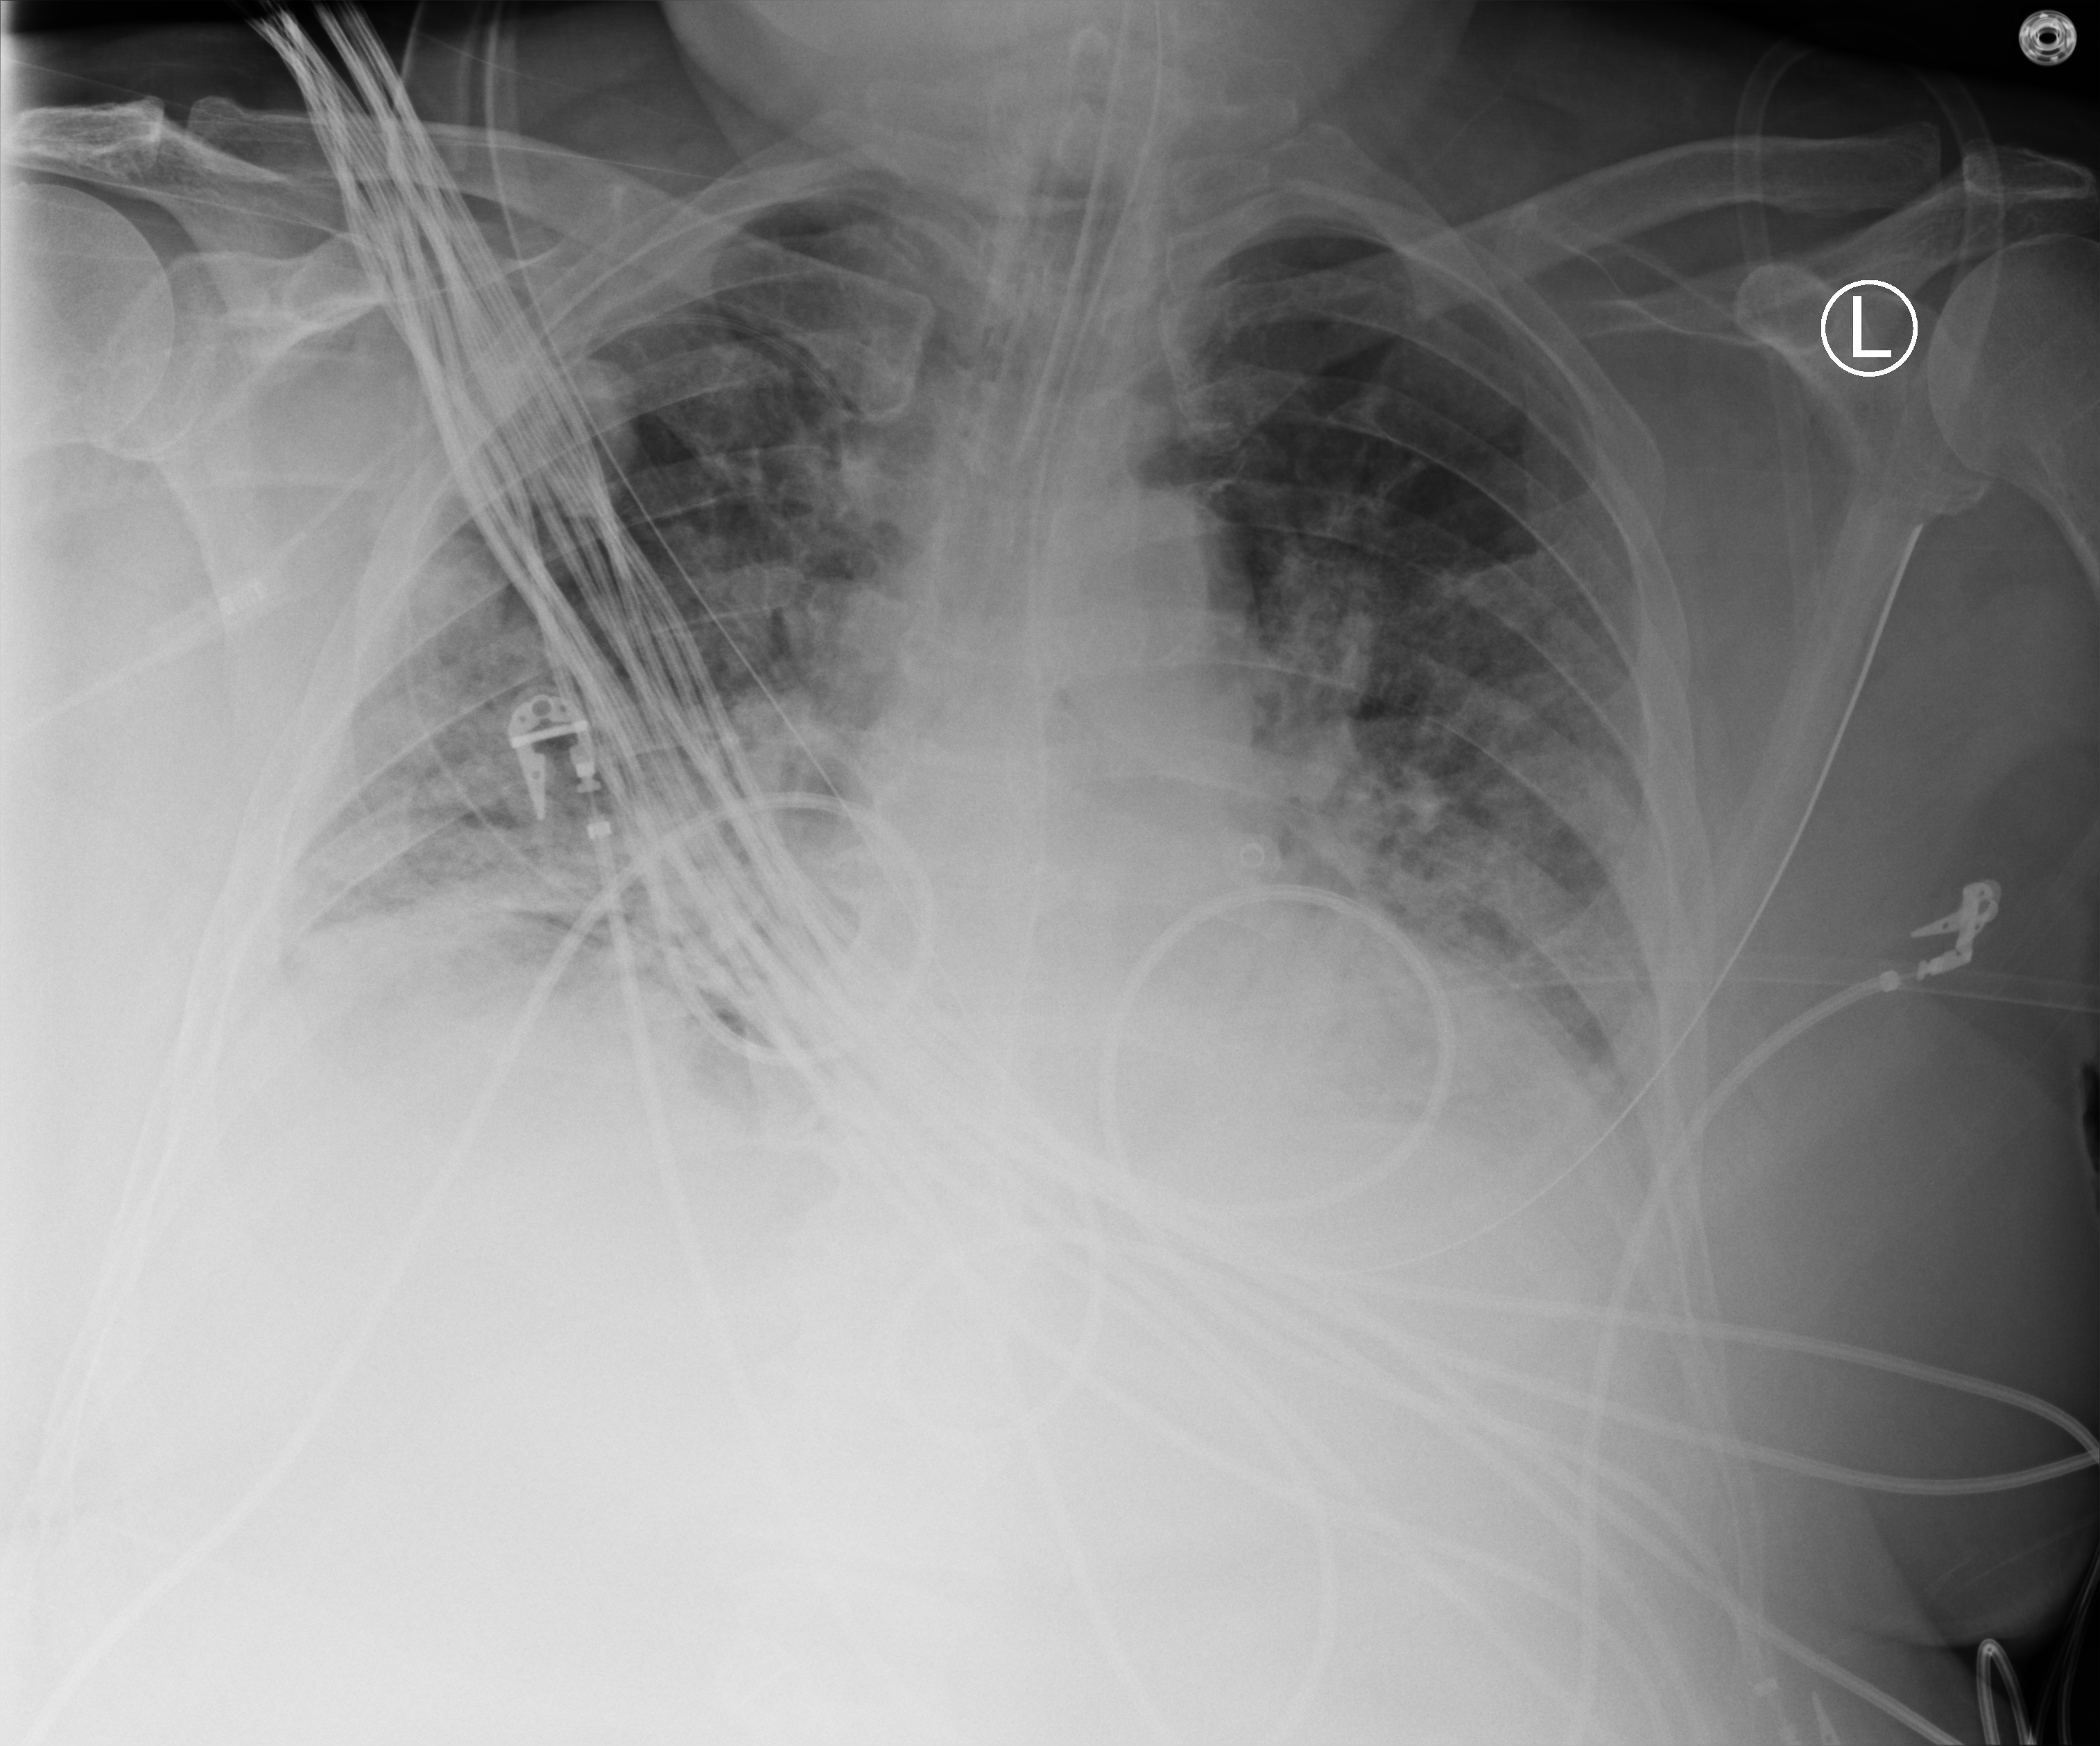
Chest X-ray (portable); anteroposterior (AP) projection. Patient hospitalised with COVID-19; male, aged 60–74 years.
Hospital-stay facts (about this admission, not read from this image; timing relative to this image not recorded): length of hospital stay: 26 days; admitted to intensive care during this hospital stay: yes; mechanically ventilated during this hospital stay: yes.